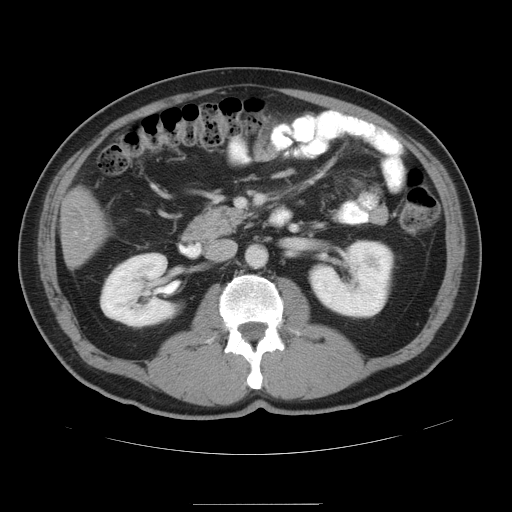
Contrast-enhanced abdominal CT, one axial slice. Slice 18 of 47 in the series (ordered by position). 120 kVp. Intravenous contrast given. Soft-tissue window (W 400 / L 40 HU). 5 mm slice thickness. 512 × 512 image matrix. Male patient, age 61 years. Case-level facts recorded for this patient, not image findings: diagnosis: colorectal cancer liver metastases, imaged before liver resection; multiple liver metastases: no; largest metastasis: 1.2 cm.
Structures marked on this image (manually delineated by an expert):
- liver: box from (x=62, y=191) to (x=107, y=266) px
- planned liver remnant (the part of the liver to remain after resection): (x=67, y=191)–(x=107, y=235)